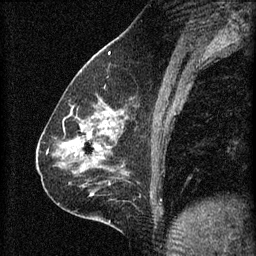
Breast MRI (dynamic contrast-enhanced), one sagittal slice. Slice 29 of 60 in the series (ordered by position). 3 images stored at this slice position (order not interpretable as contrast timing). 1.5 T. TE 4.2 ms, TR 8.2 ms. 2 mm slice thickness. 256 × 256 image matrix. Female patient, age 59 years.
Structures marked on this image (semi-automatic segmentation, software-assisted and operator-edited):
- analysis volume of interest (the breast-tissue region the enhancement analysis was run in; not a lesion): bounding box [x1, y1, x2, y2] px = [61, 104, 130, 161]
- tumour enhancement mask (voxels above the 70 % enhancement threshold inside the analysis volume of interest): [65, 112, 124, 157]